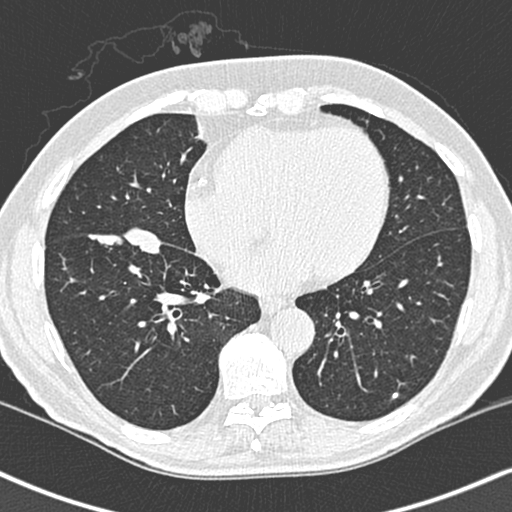
Low-dose screening chest CT, one axial slice. Position 106 of 248 along the scan axis. 120 kVp. Lung window (W 1500 / L -600 HU). 512 × 512 image matrix, field of view 323 × 323 mm.
Outlined on this slice (manually delineated by an expert):
- lesion 1 (tumor, lower lobe of right lung): bounding box (x1, y1, x2, y2) in pixels: (88, 190, 163, 216)